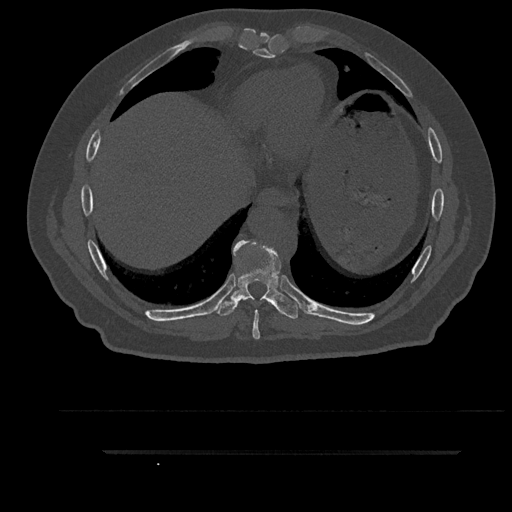
CT including the spine, one axial slice; position 442 of 797 along the scan axis; reconstruction kernel Br40s/3; bone window (W 1800 / L 400 HU); 512 × 512 image matrix, field of view 432 × 432 mm. Male patient, age 63 years. From the clinical record (not read from this slice): primary cancer: renal; vertebrae with lytic lesions (as recorded): T8.
Annotated regions visible in this slice (semi-automatically segmented with operator editing):
- T8 vertebra: bounding box [x1, y1, x2, y2] px = [234, 241, 274, 339]
- T9 vertebra: [213, 240, 299, 319]